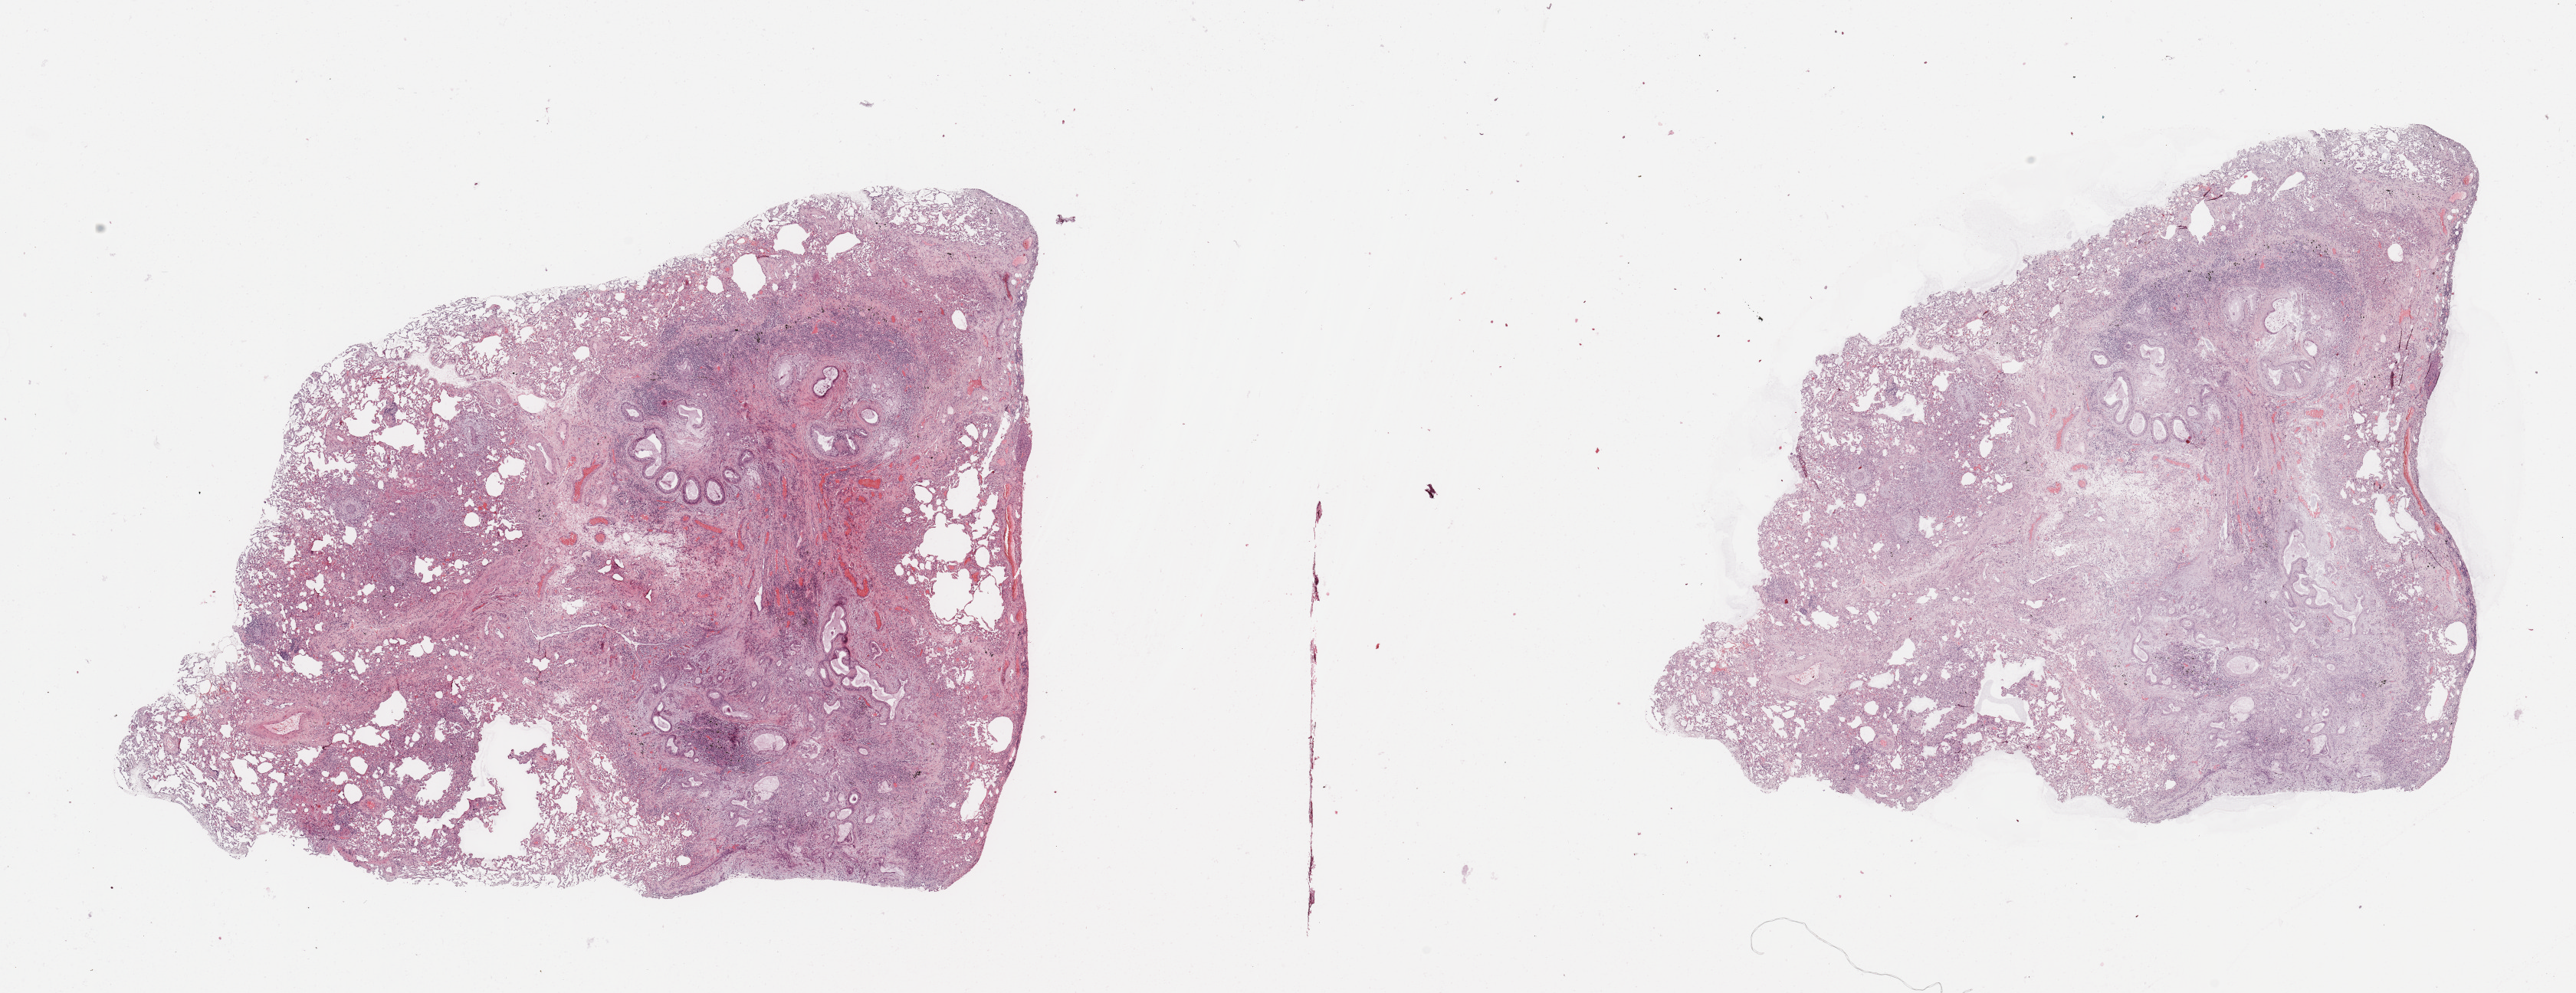
Digitized H&E tissue section (whole slide), a low-resolution overview of the entire scanned area, about 26.6 x 10.2 mm, lung, tissue type not recorded.
Patient diagnosis (cohort enrolment): lung adenocarcinoma (lung).